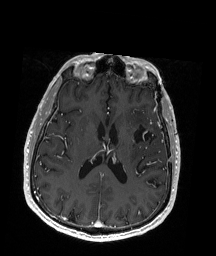
Brain MRI from a brain-tumour surgery series, one axial slice; slice 85 of 192 in the series (ordered by position); T1-weighted post-contrast; 1 mm slice thickness; 216 × 256 image matrix. From the clinical record (not read from this slice): histopathology: Oligodendroglioma; WHO grade: 2; IDH mutation: yes; tumour location: Left Insular.
Annotated regions visible in this slice (expert manual segmentation):
- previous resection cavity: box from (x=132, y=121) to (x=163, y=141) px